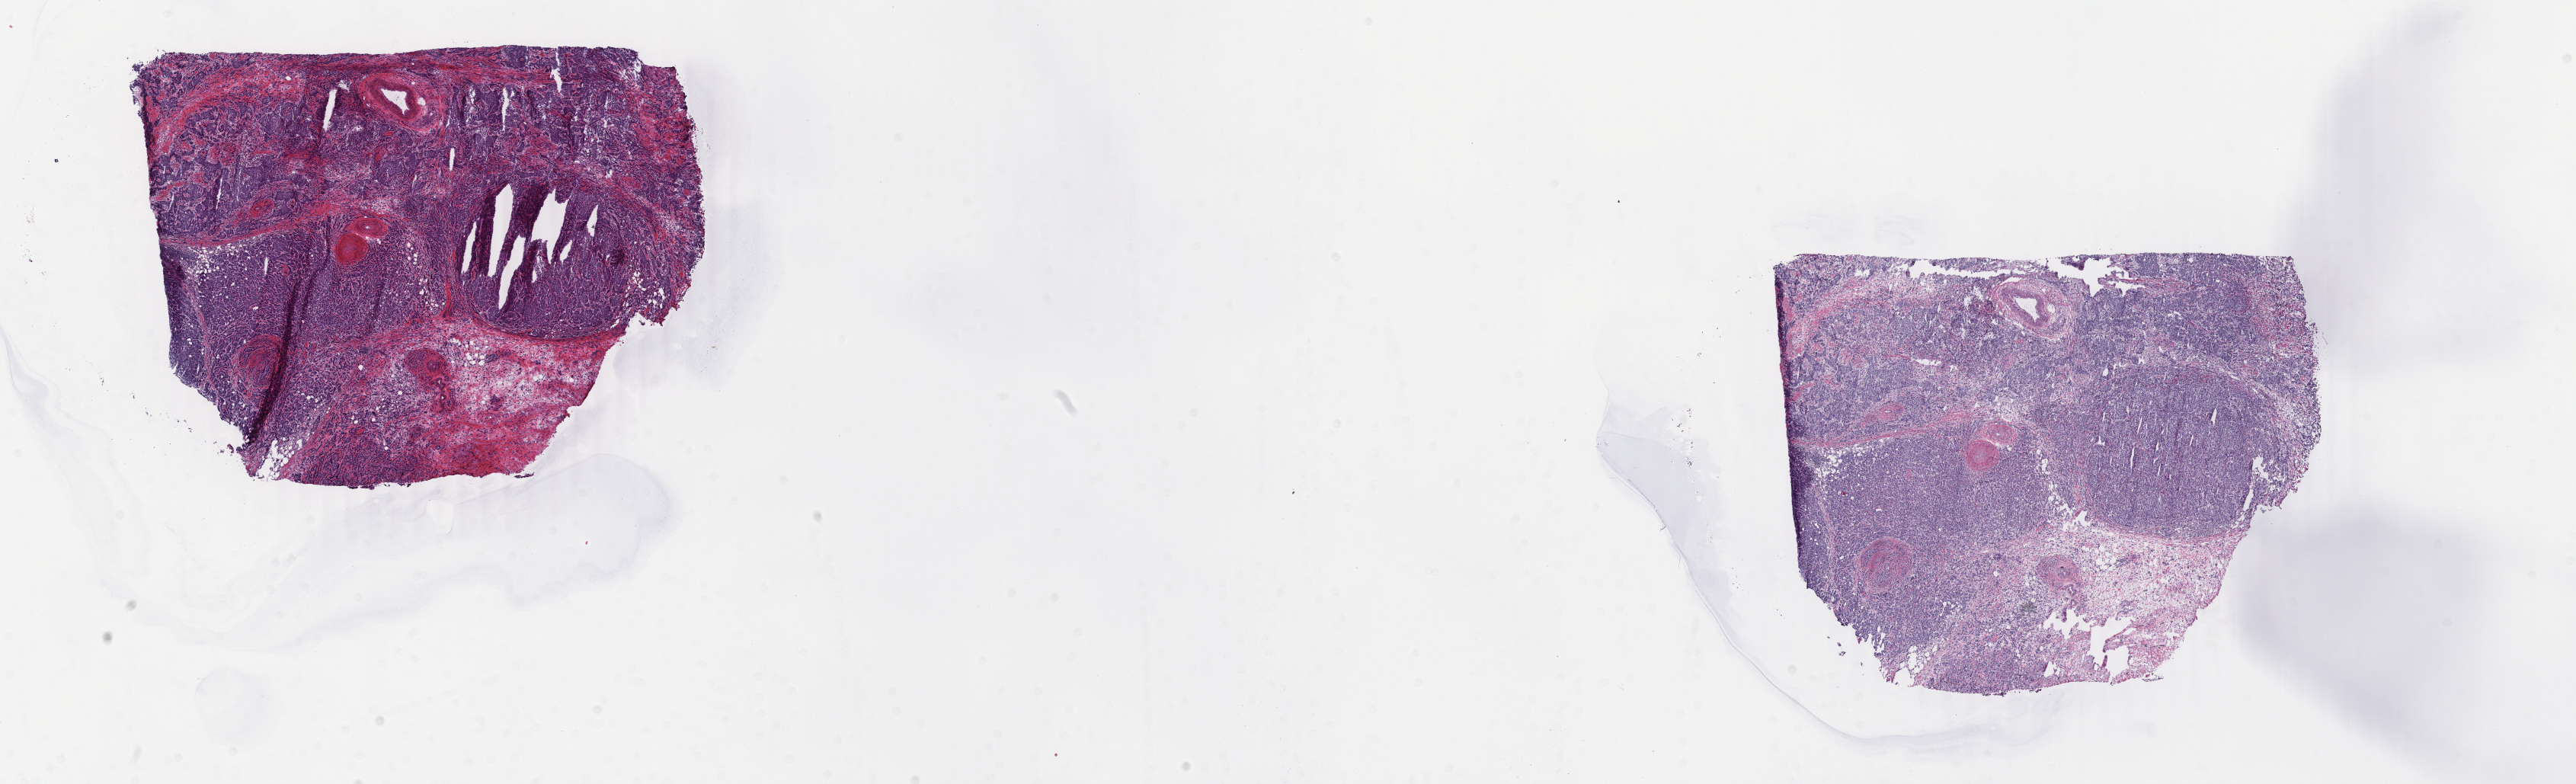
Digitized Hematoxylin and eosin (H&E) stained tissue section (whole slide), whole scanned area (about 26.9 x 8.2 mm) shown as a low-resolution overview; frozen section; breast, primary tumour sample. Patient: female, age at initial diagnosis 62 years. Composition of this section per pathologist review: tumour cells 85%, tumour nuclei 95%, normal cells 0%, stromal cells 14%, necrosis 1%. Inflammatory infiltration, as recorded: lymphocyte infiltration 4%, monocyte infiltration 0%, neutrophil infiltration 0%.
* laterality: left
* TNM: T2 N1a M0
* lymph nodes positive (case pathology): 1 of 15 examined
* AJCC pathologic stage: IIB (7th edition)
* pathologic diagnosis: Infiltrating duct carcinoma, NOS